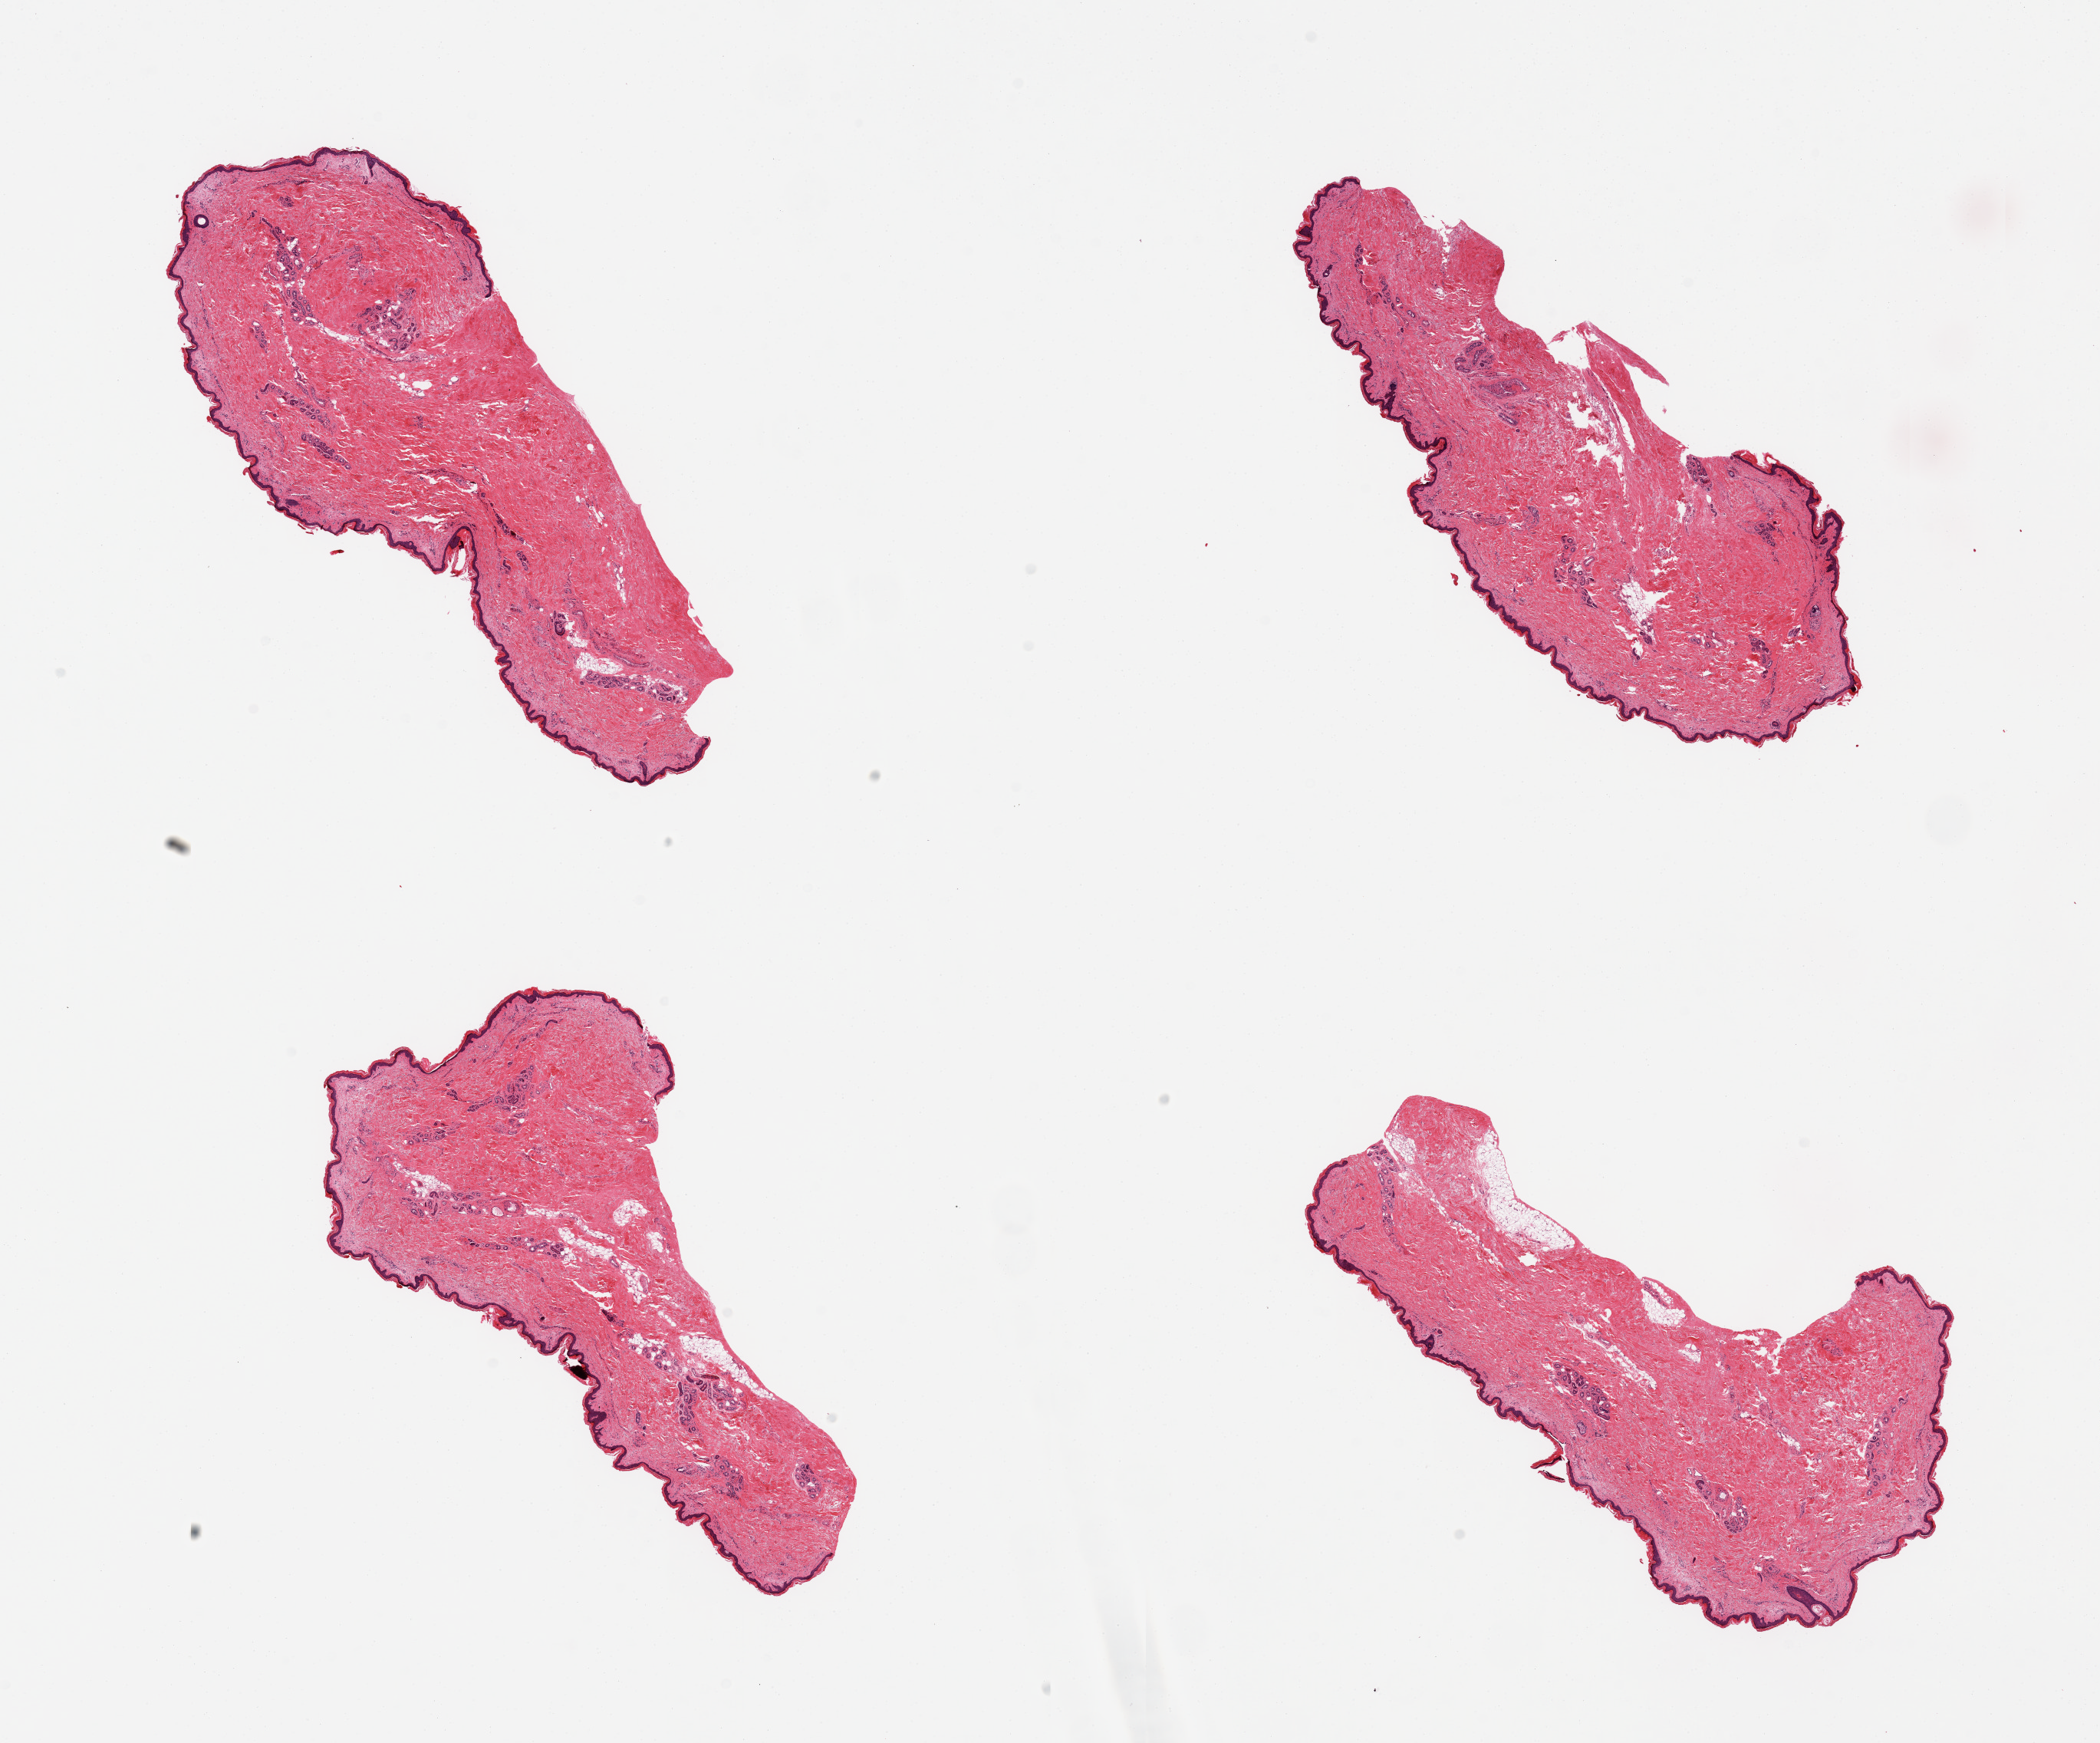
Digitized haematoxylin and eosin-stained section — shown as a low-resolution overview of the whole scanned area (about 21.7 x 18.0 mm, slide scanned at 20x). PAXgene-fixed, paraffin-embedded tissue. Sampled site (target tissue): skin of lower leg. Tissue donor sample. Male donor.
Pathologist's review note for this sample: 4 pieces, well trimmed, minimal fat, squamous epithelium measures 23 to 36 microns.